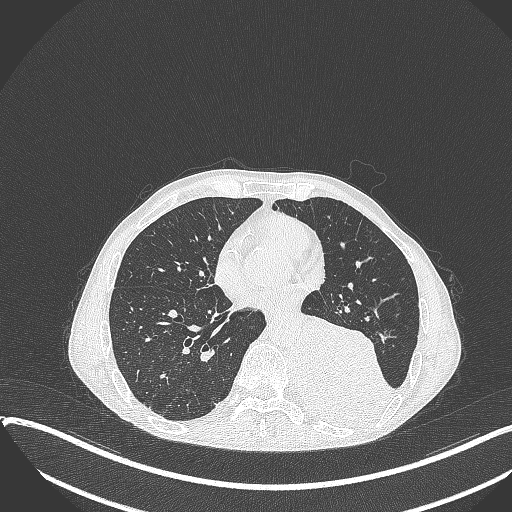
Chest CT, one axial slice. Position 150 of 401 along the scan axis. Reconstruction kernel B70f. 120 kVp. Lung window (W 1500 / L -600 HU). 512 × 512 image matrix. Male patient, age 57 years. Case-level facts recorded for this patient, not image findings: clinical TNM (as recorded): T4 N0 M0.
Structures marked on this image (rectangle marked by the reading radiologist):
- lung tumour (recorded histology: squamous cell carcinoma): box from (x=297, y=313) to (x=394, y=430) px